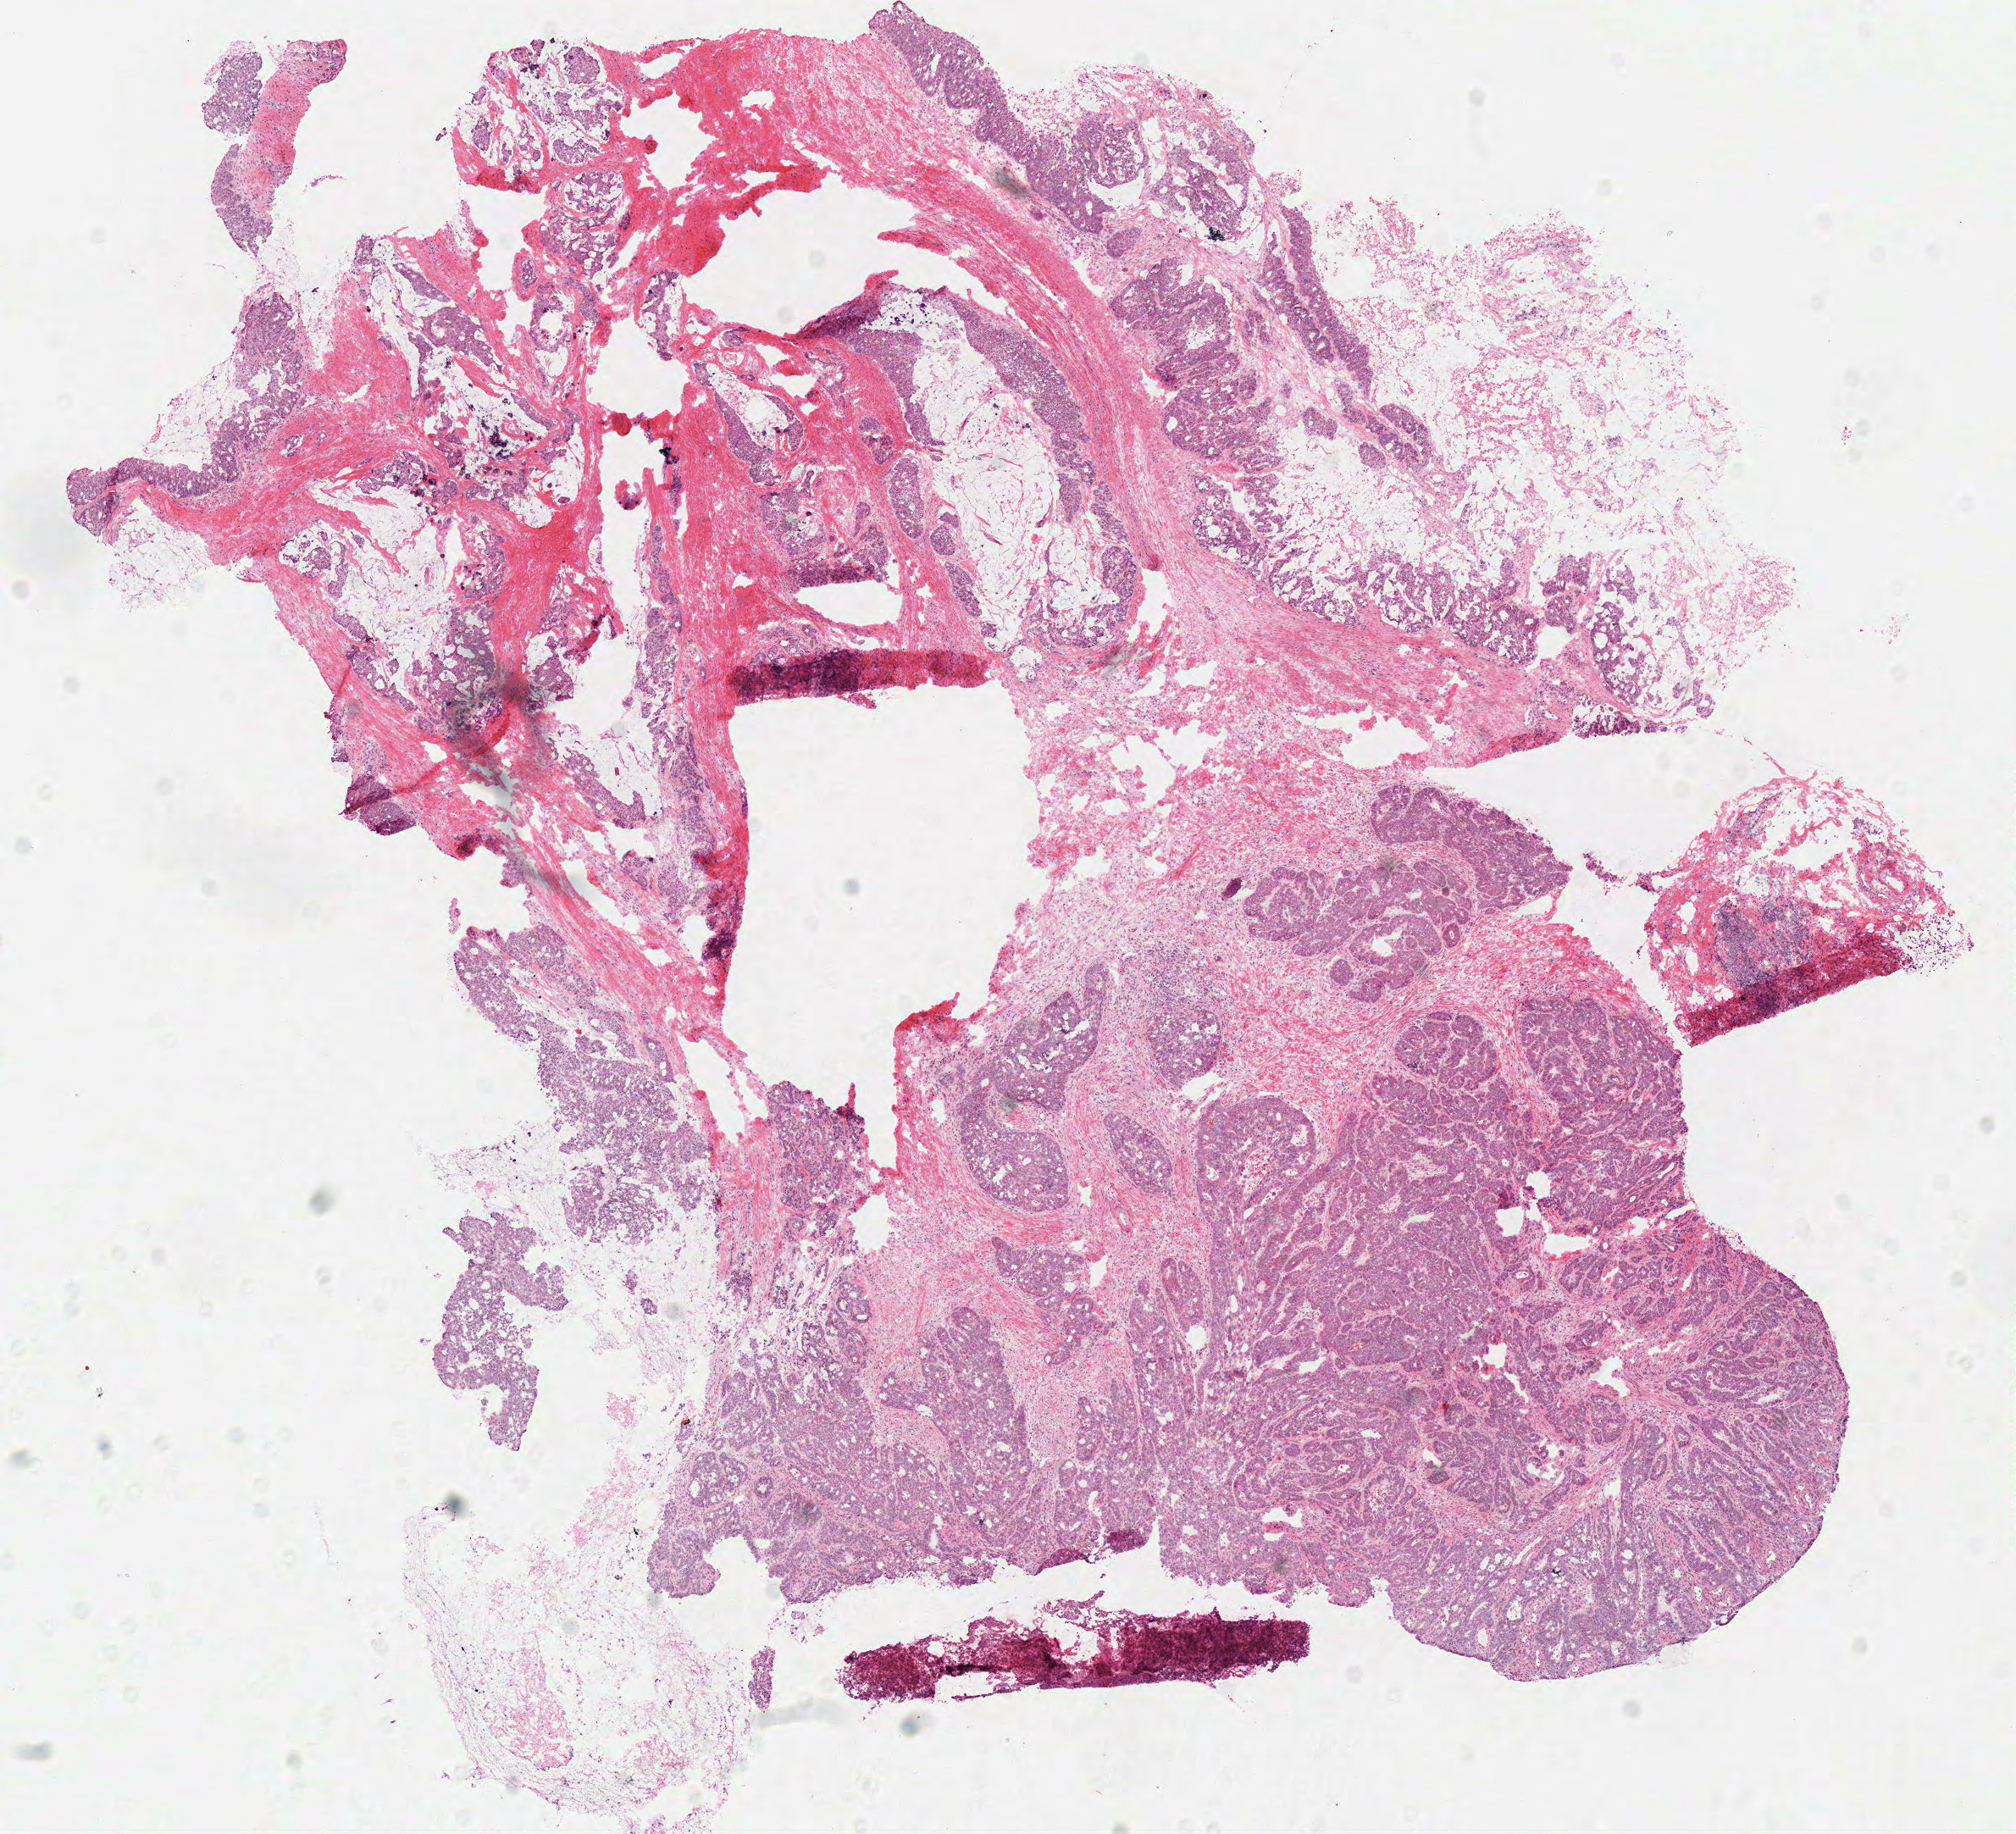
Digitized H&E-stained tissue section (whole slide), a low-resolution overview of the entire scanned area, about 9.4 x 8.5 mm (acquisition: 40x scan), frozen section from the top of the tissue portion, primary tumour sample from the colon. Male, age 74 years at initial diagnosis. Composition of this section per pathologist review: tumour cells 58%, tumour nuclei 80%, normal cells 2%, stromal cells 20%, necrosis 20%.
AJCC pathologic stage: IIA (7th edition). Lymph nodes positive (case pathology): 0 of 20 examined. Histologic diagnosis: Adenocarcinoma, NOS (sigmoid colon).